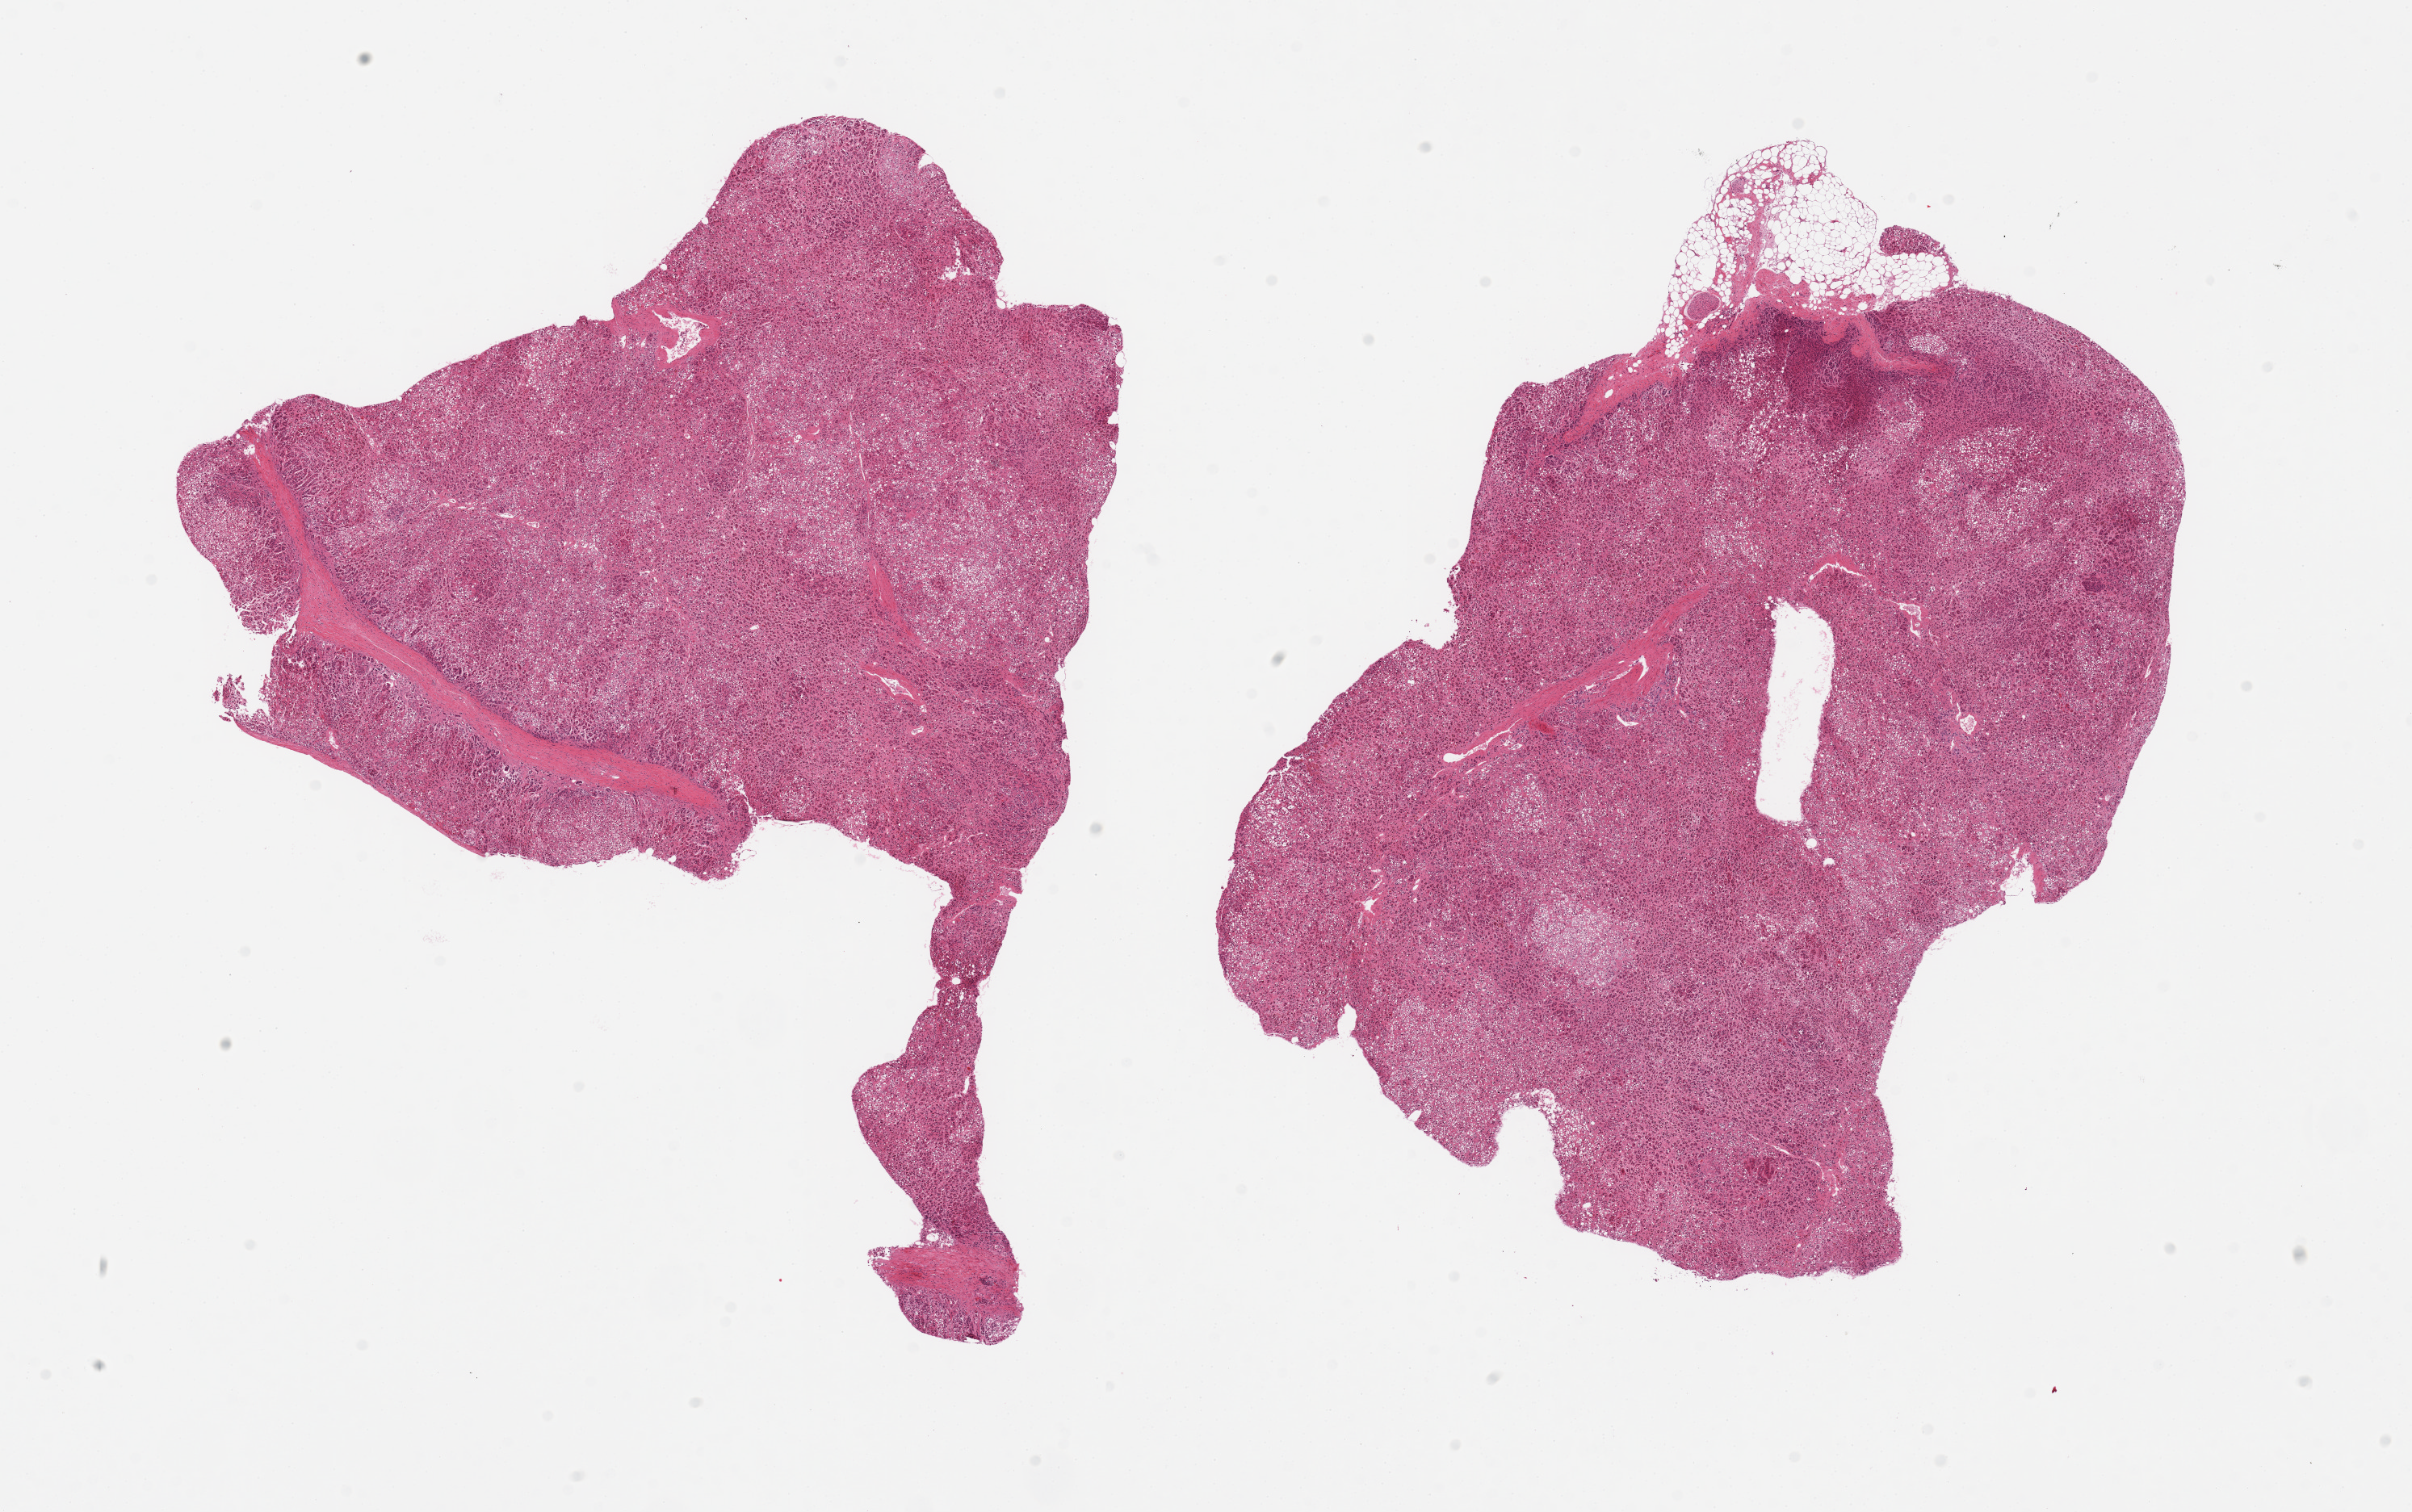
Whole-slide image, haematoxylin and eosin stain — low-resolution overview of the scanned area, about 23.6 x 14.8 mm (acquisition: 20x scan), PAXgene-fixed, paraffin-embedded tissue, target tissue: adrenal gland, donor tissue sample. Male donor.
- reviewer comment on this tissue sample: 2 pieces all cortex, intermingled fat